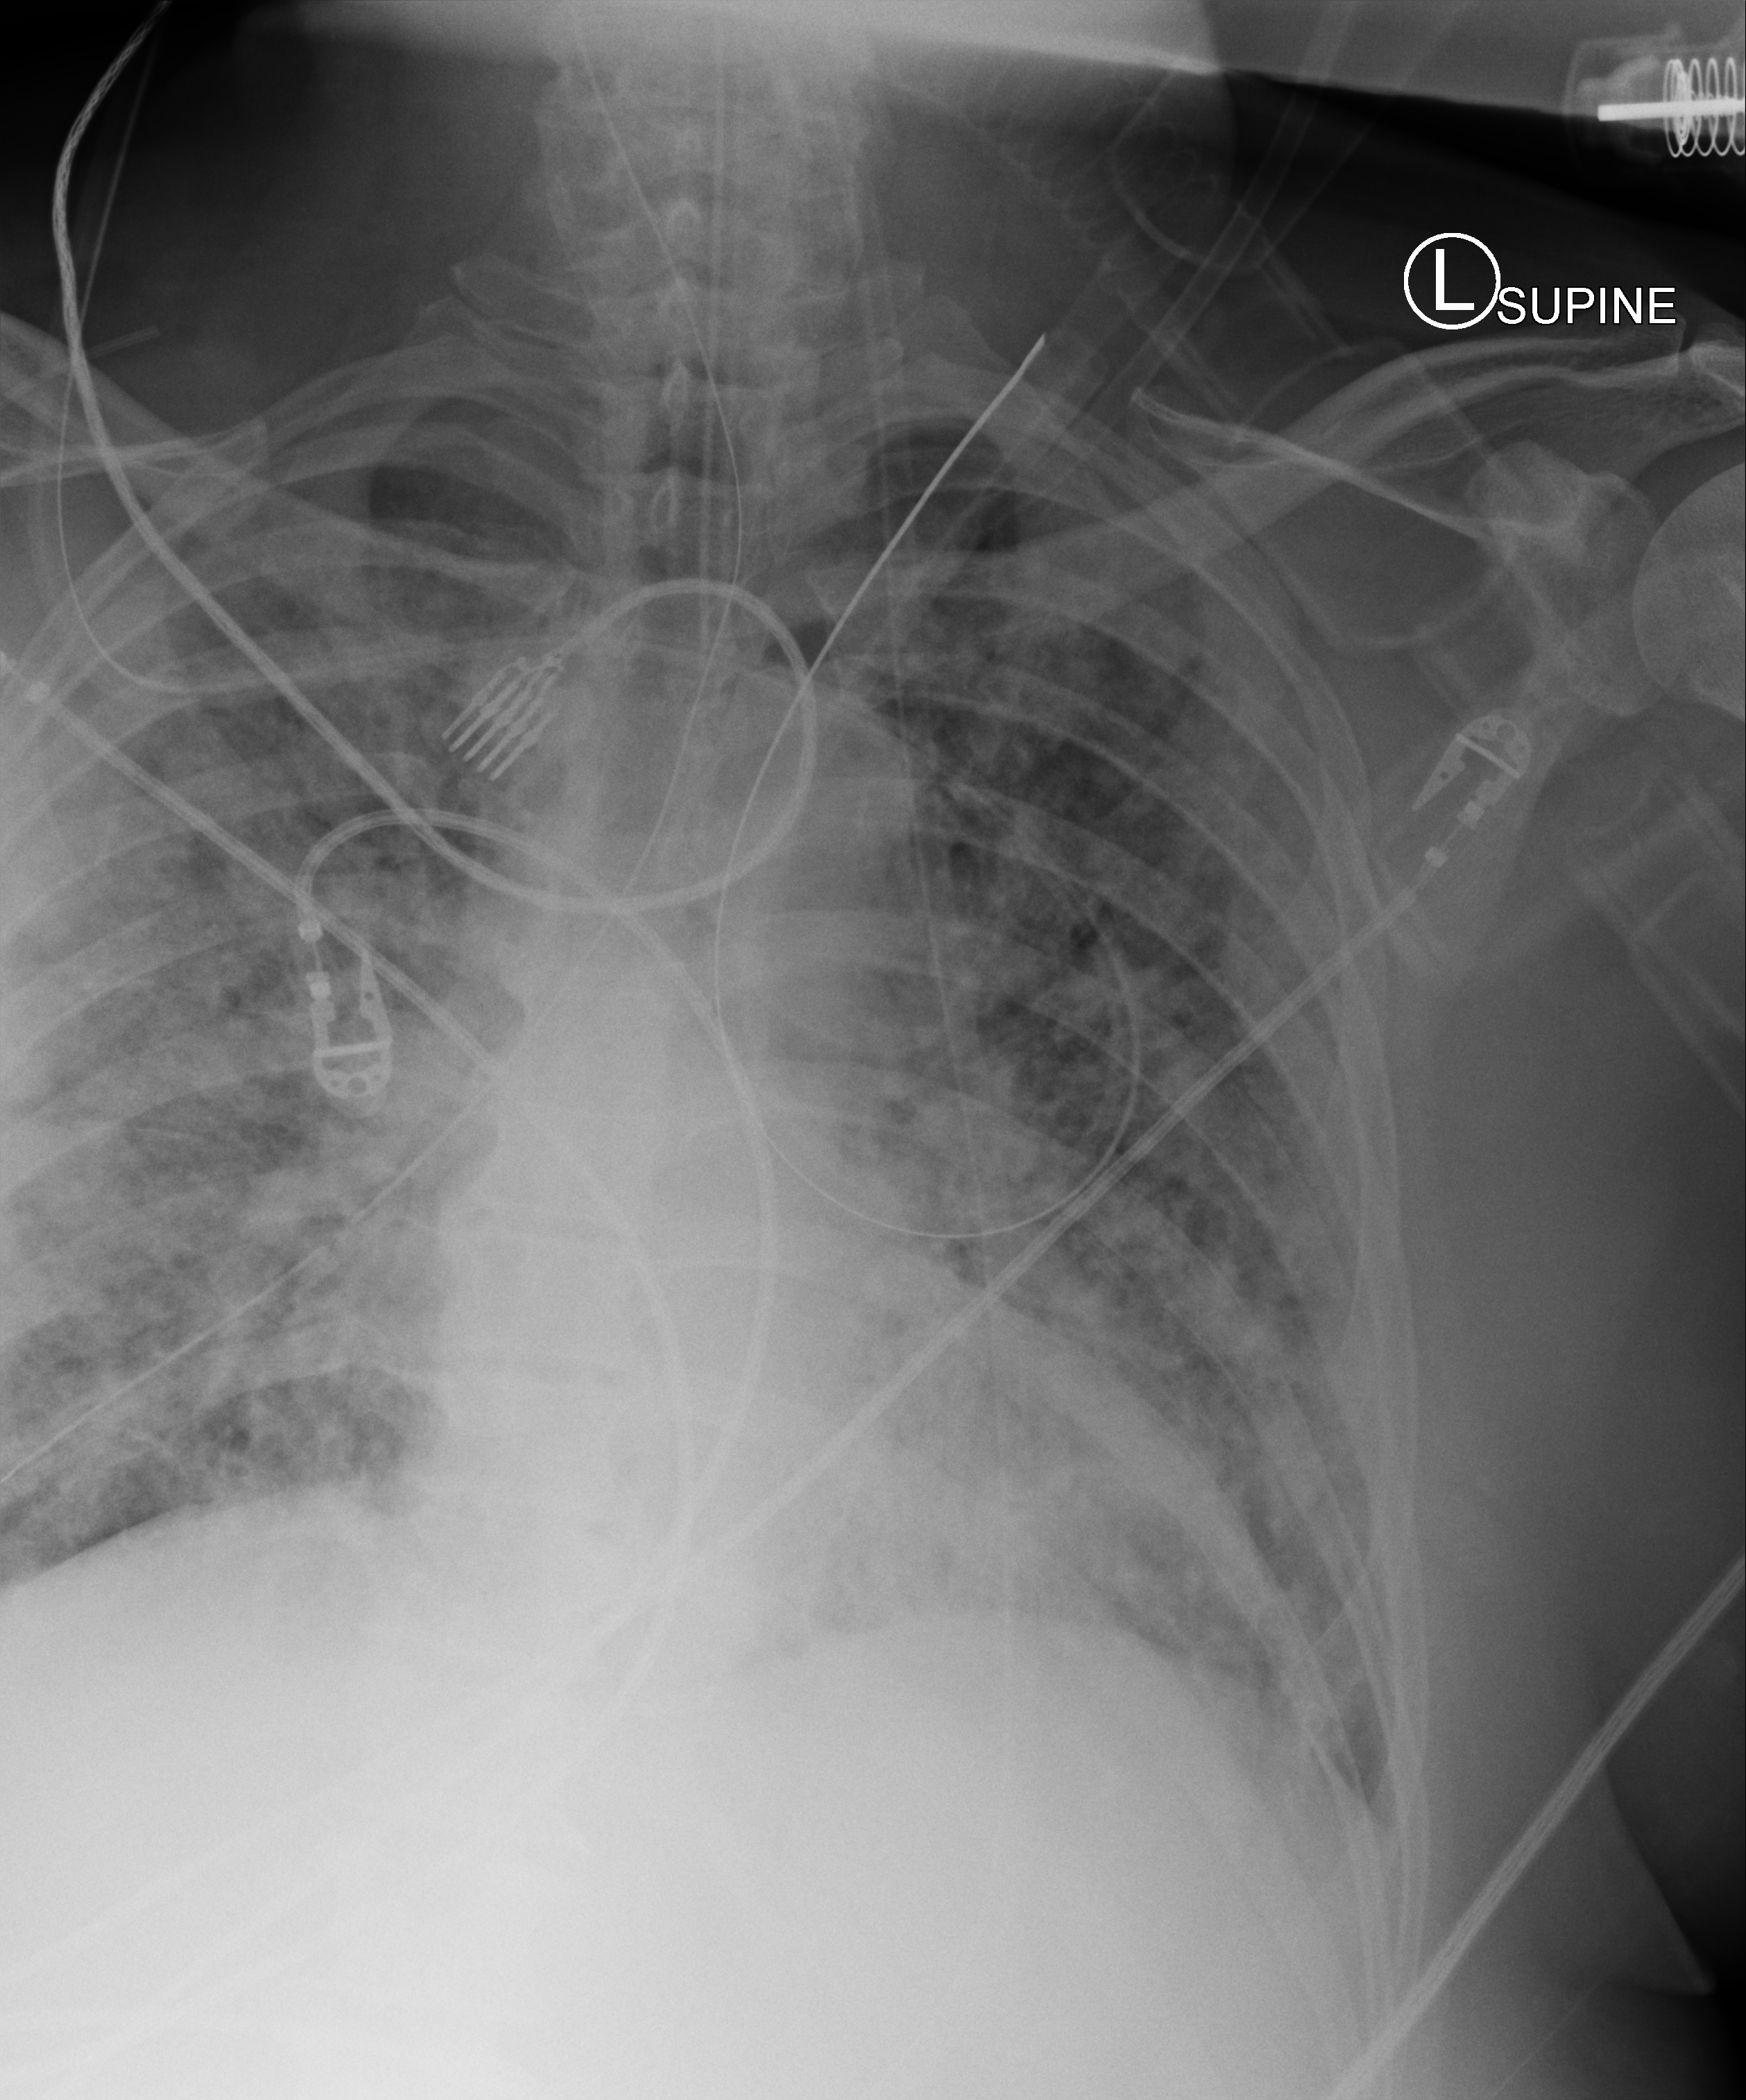
Portable chest radiograph, anteroposterior (AP) projection. Male patient hospitalised with COVID-19, age 60–74 years.
Admission-level facts for this patient (not findings on this image; timing relative to this image not recorded):
- admitted to intensive care during this hospital stay: yes
- mechanically ventilated during this hospital stay: yes